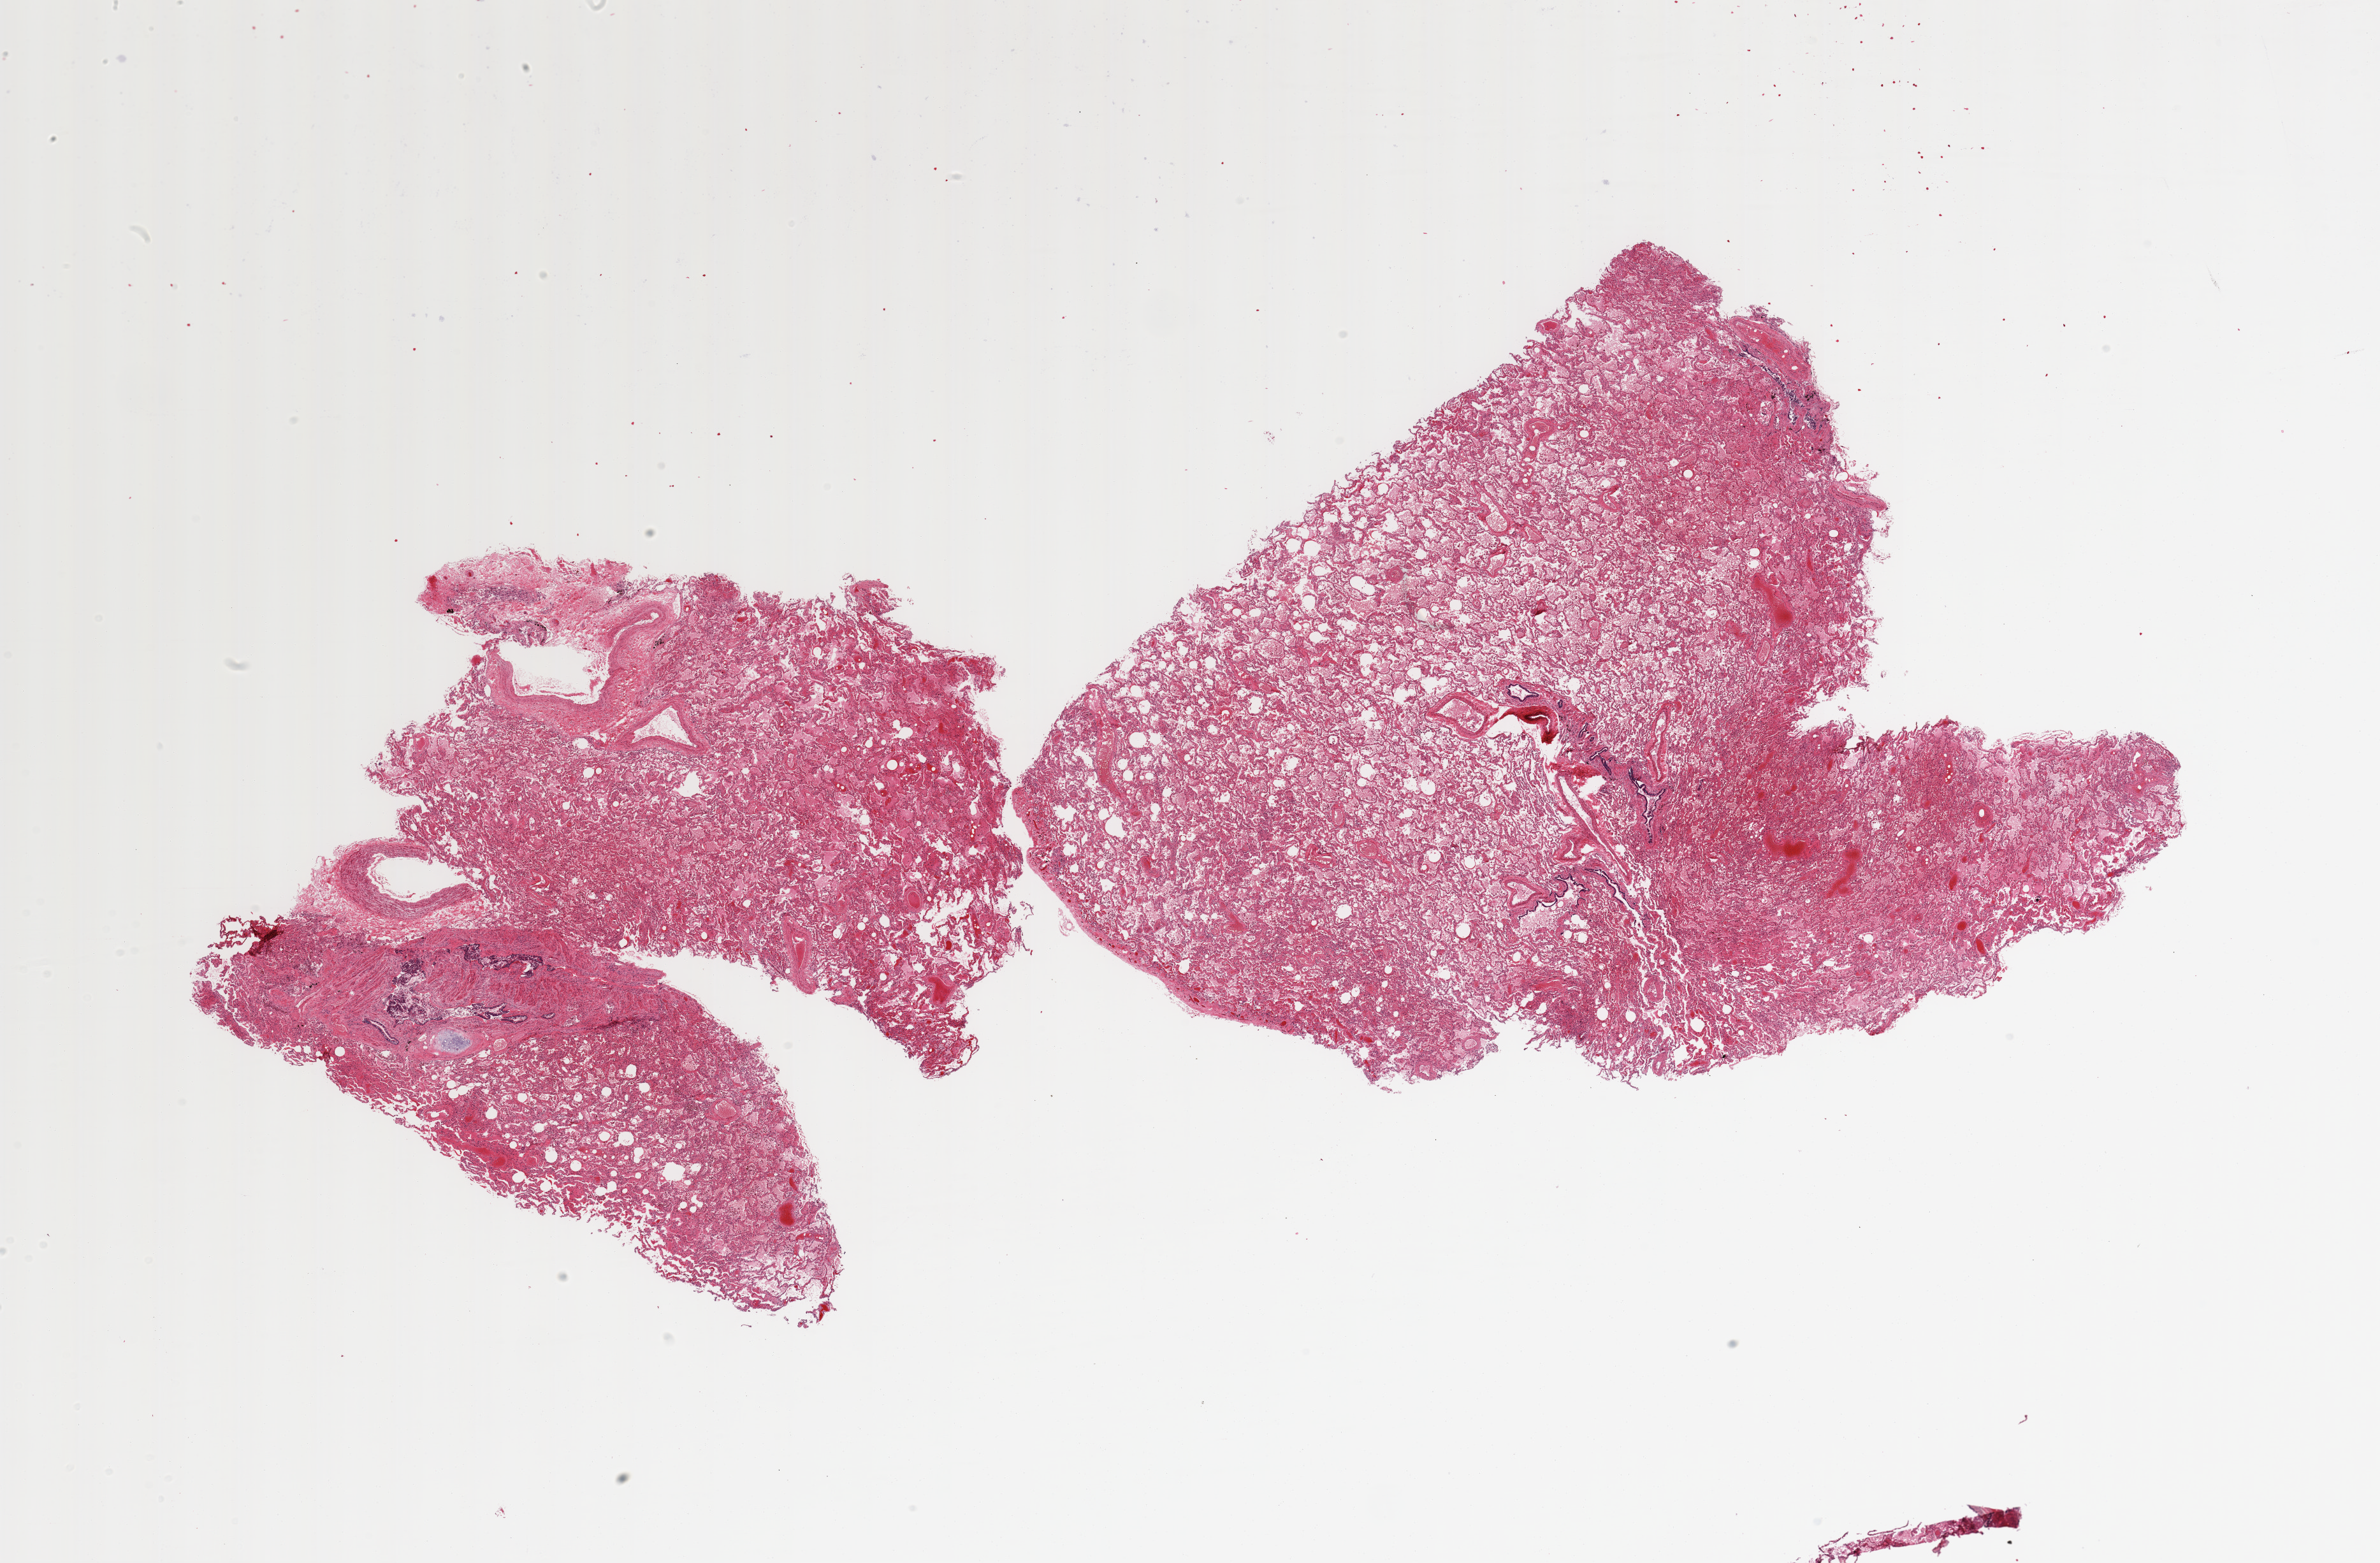
Whole-slide image, hematoxylin and eosin (H&E) stain, whole scanned area (about 29.5 x 19.4 mm) shown as a low-resolution overview, PAXgene-fixed, paraffin-embedded tissue, section of lung (target tissue), donor tissue sample. Donor: male.
Reviewer comment on this tissue sample: 2 pieces; severe congestion; bronchial wall and desquamated bronchial epithelium and fragment of cartilage; anthracosis; thick walled pulmonary vessels; focal pleural coverage.